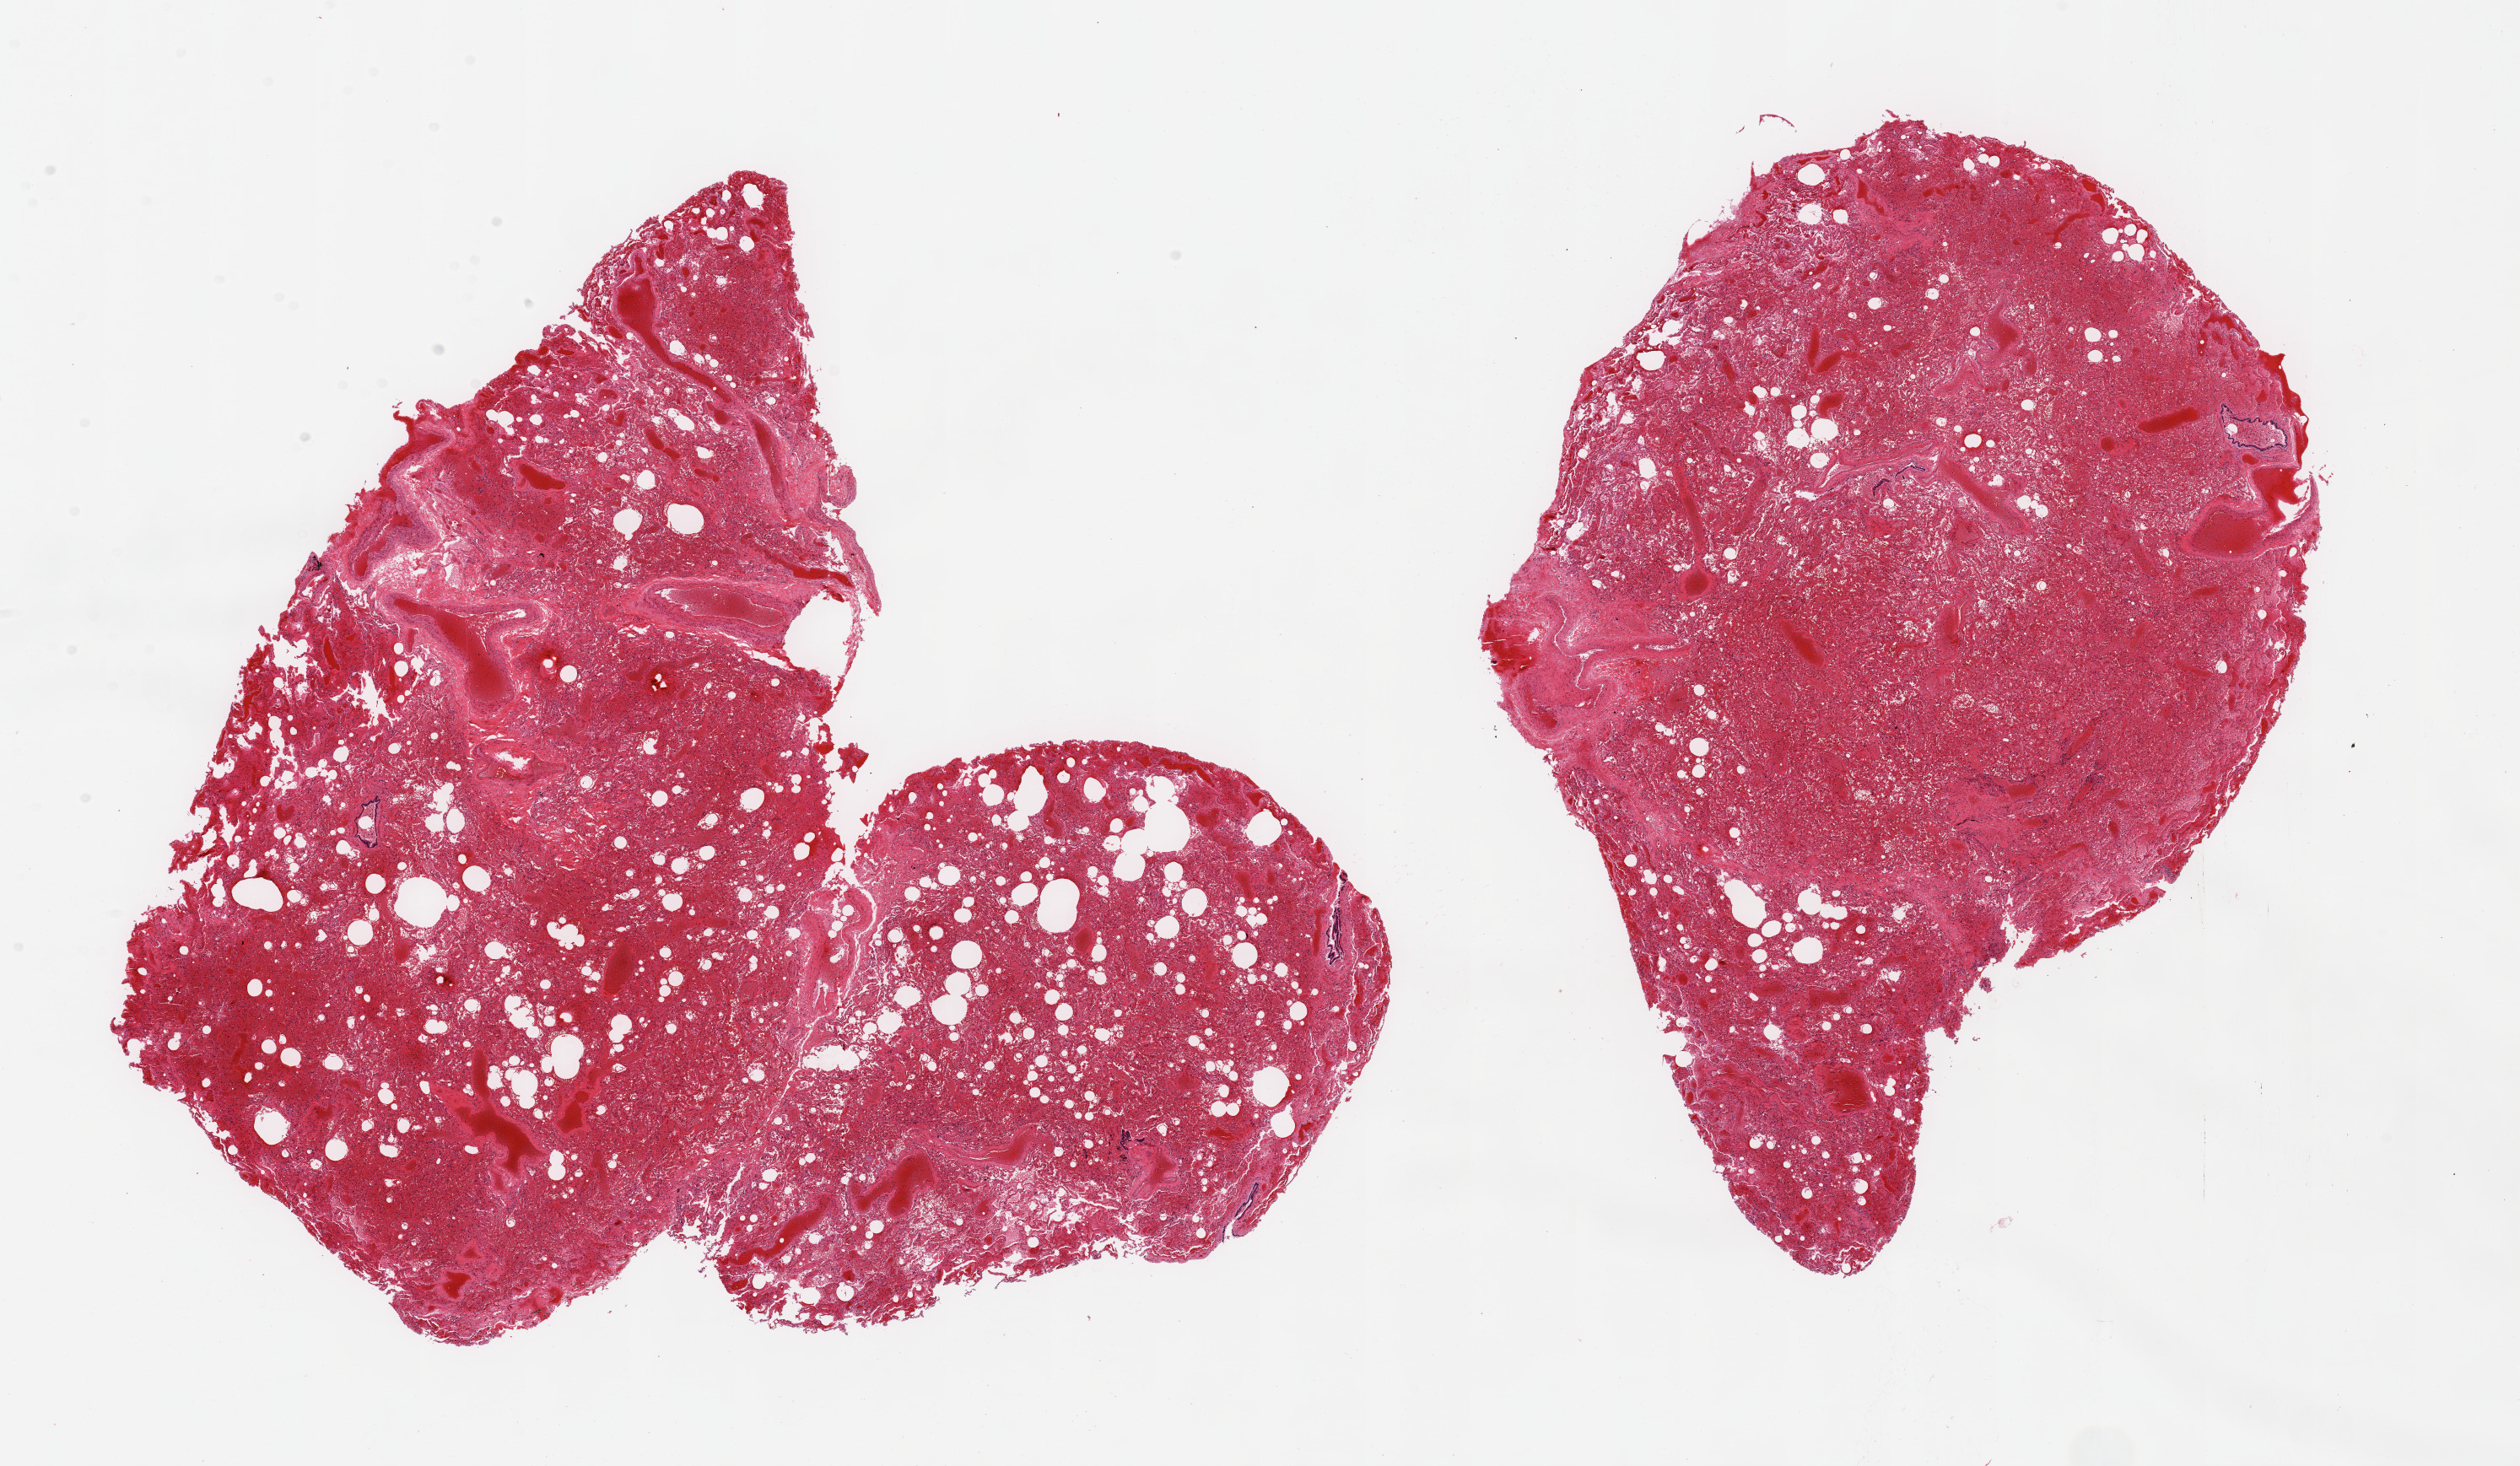
Whole-slide image, haematoxylin and eosin stain, brightfield, whole scanned area (about 23.6 x 13.7 mm) shown as a low-resolution overview, PAXgene-fixed paraffin-embedded (PFPE) section, sampled site (target tissue): lung, tissue donor sample. Donor sex: male.
Pathologist's review note for this sample: 2 pieces; severe congestion and fresh hemorrhage; few larger vessels.